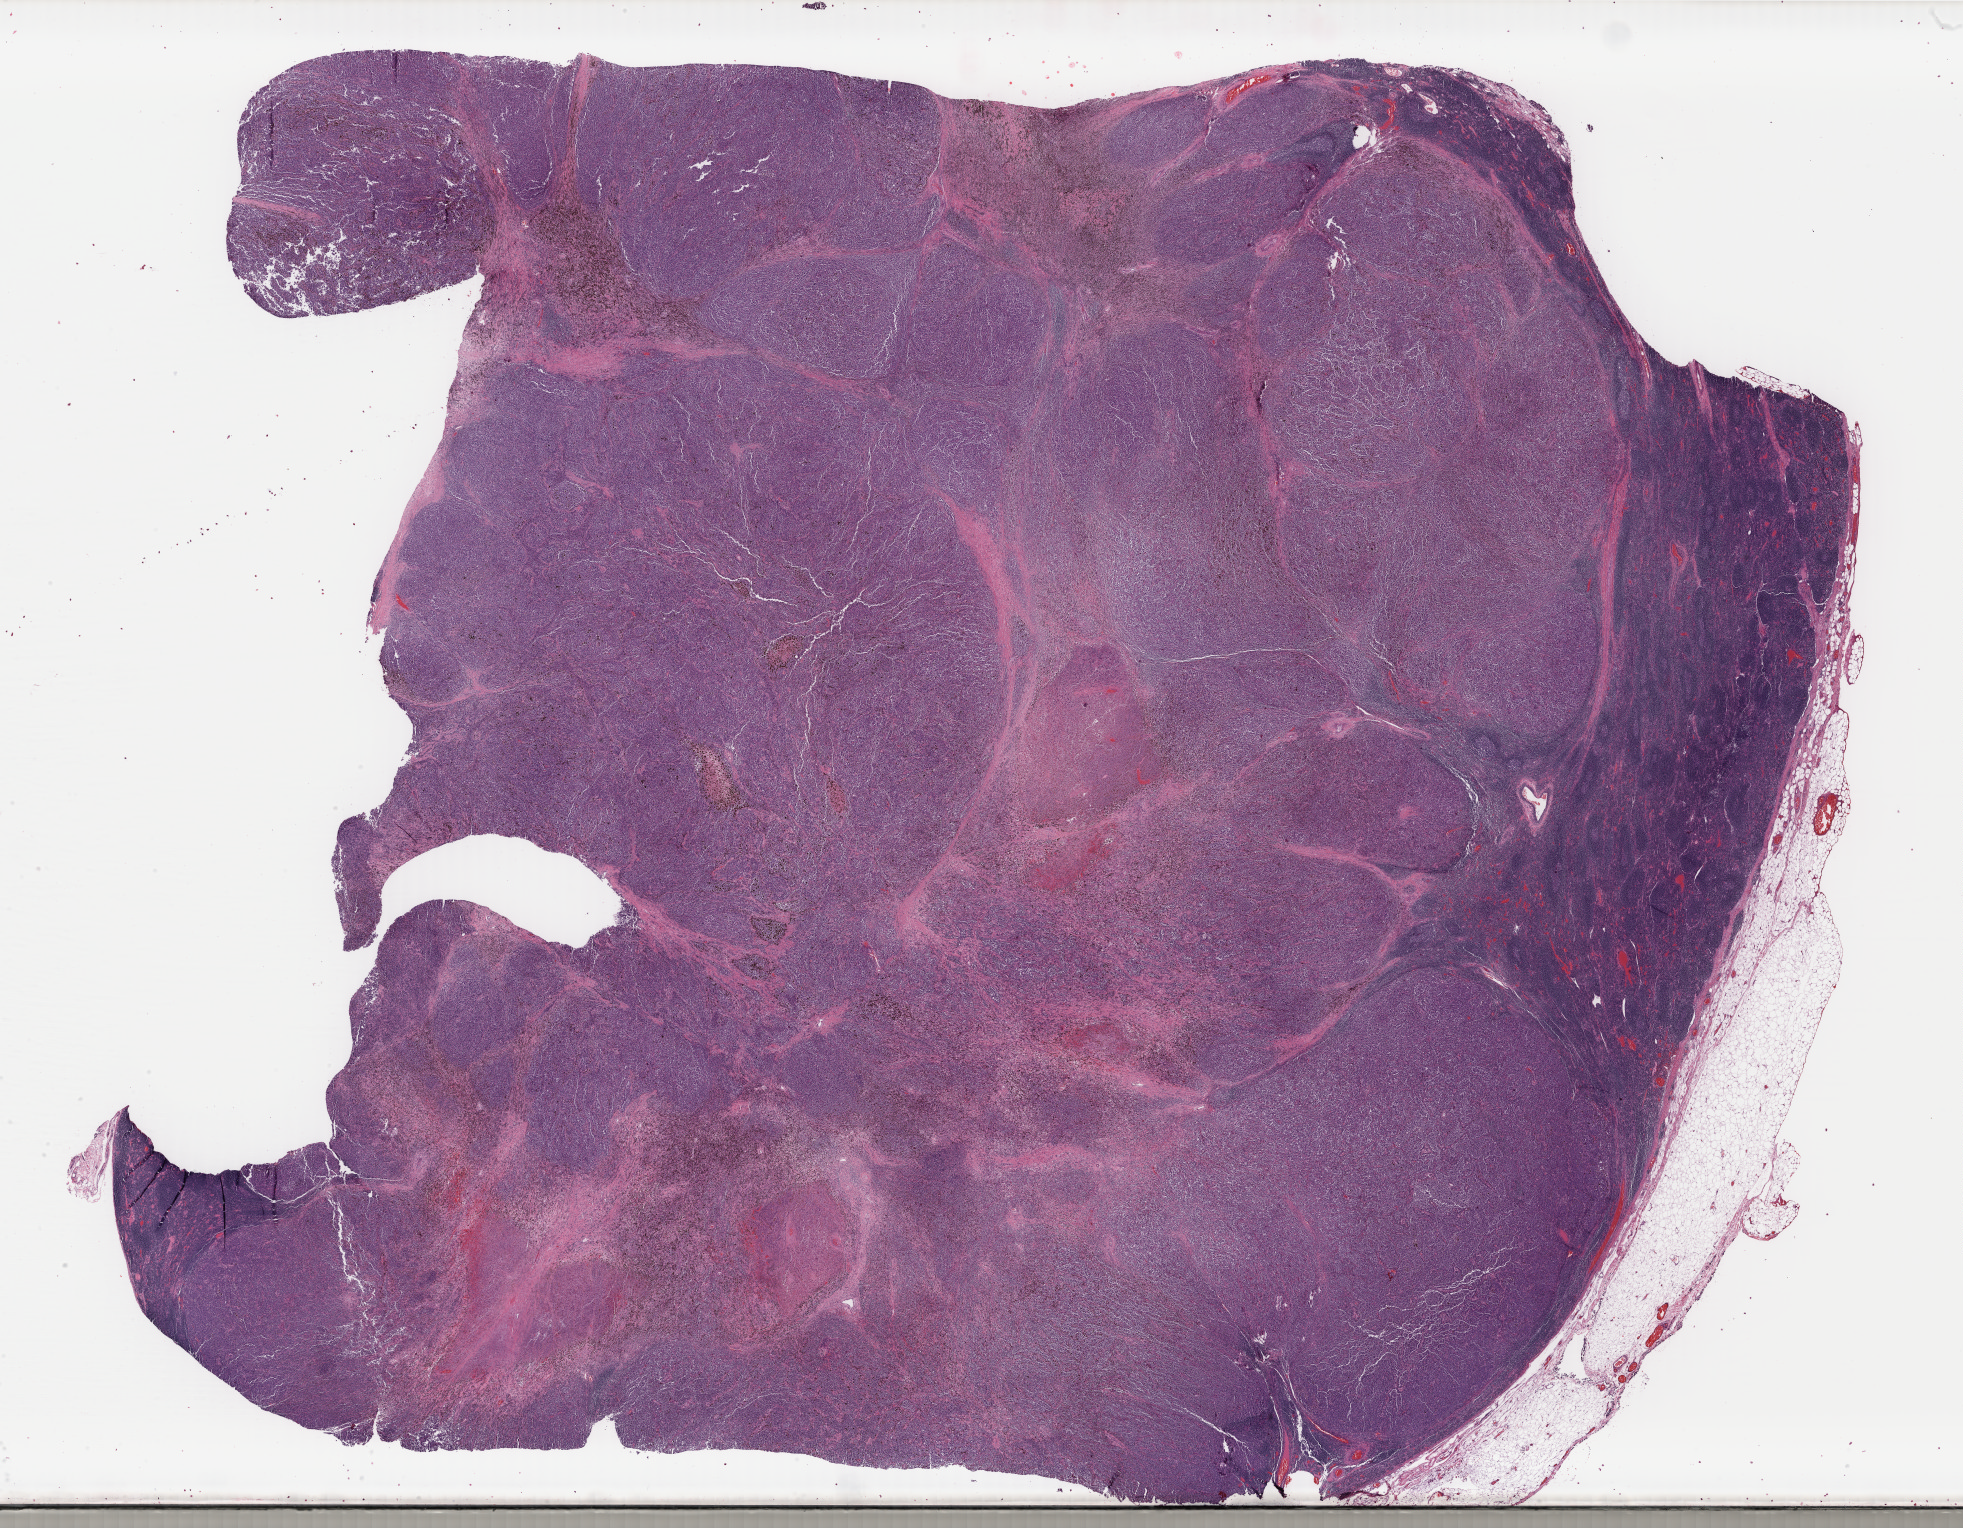
Hematoxylin and eosin (H&E) stained whole-slide image, shown as a low-resolution overview of the whole scanned area (about 31.2 x 24.3 mm), formalin-fixed paraffin-embedded (FFPE) diagnostic section, primary tumour sample from the skin. Male patient; age at initial diagnosis 47 years.
• histologic diagnosis: Malignant melanoma, NOS